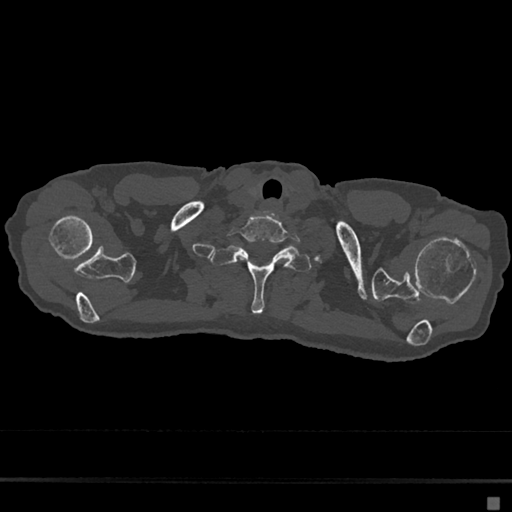
CT including the spine, one axial slice; slice 622 of 797 in the series (ordered by position); reconstruction kernel Br40s/3; 120 kVp; bone window (W 1800 / L 400 HU); 512 × 512 image matrix, field of view 360 × 360 mm. Female patient, age 68 years. Case-level facts recorded for this patient, not image findings: primary cancer: renal.
Annotated regions visible in this slice (semi-automatically segmented with operator editing):
- T1 vertebra: bounding box (x1, y1, x2, y2) in pixels: (210, 246, 312, 314)